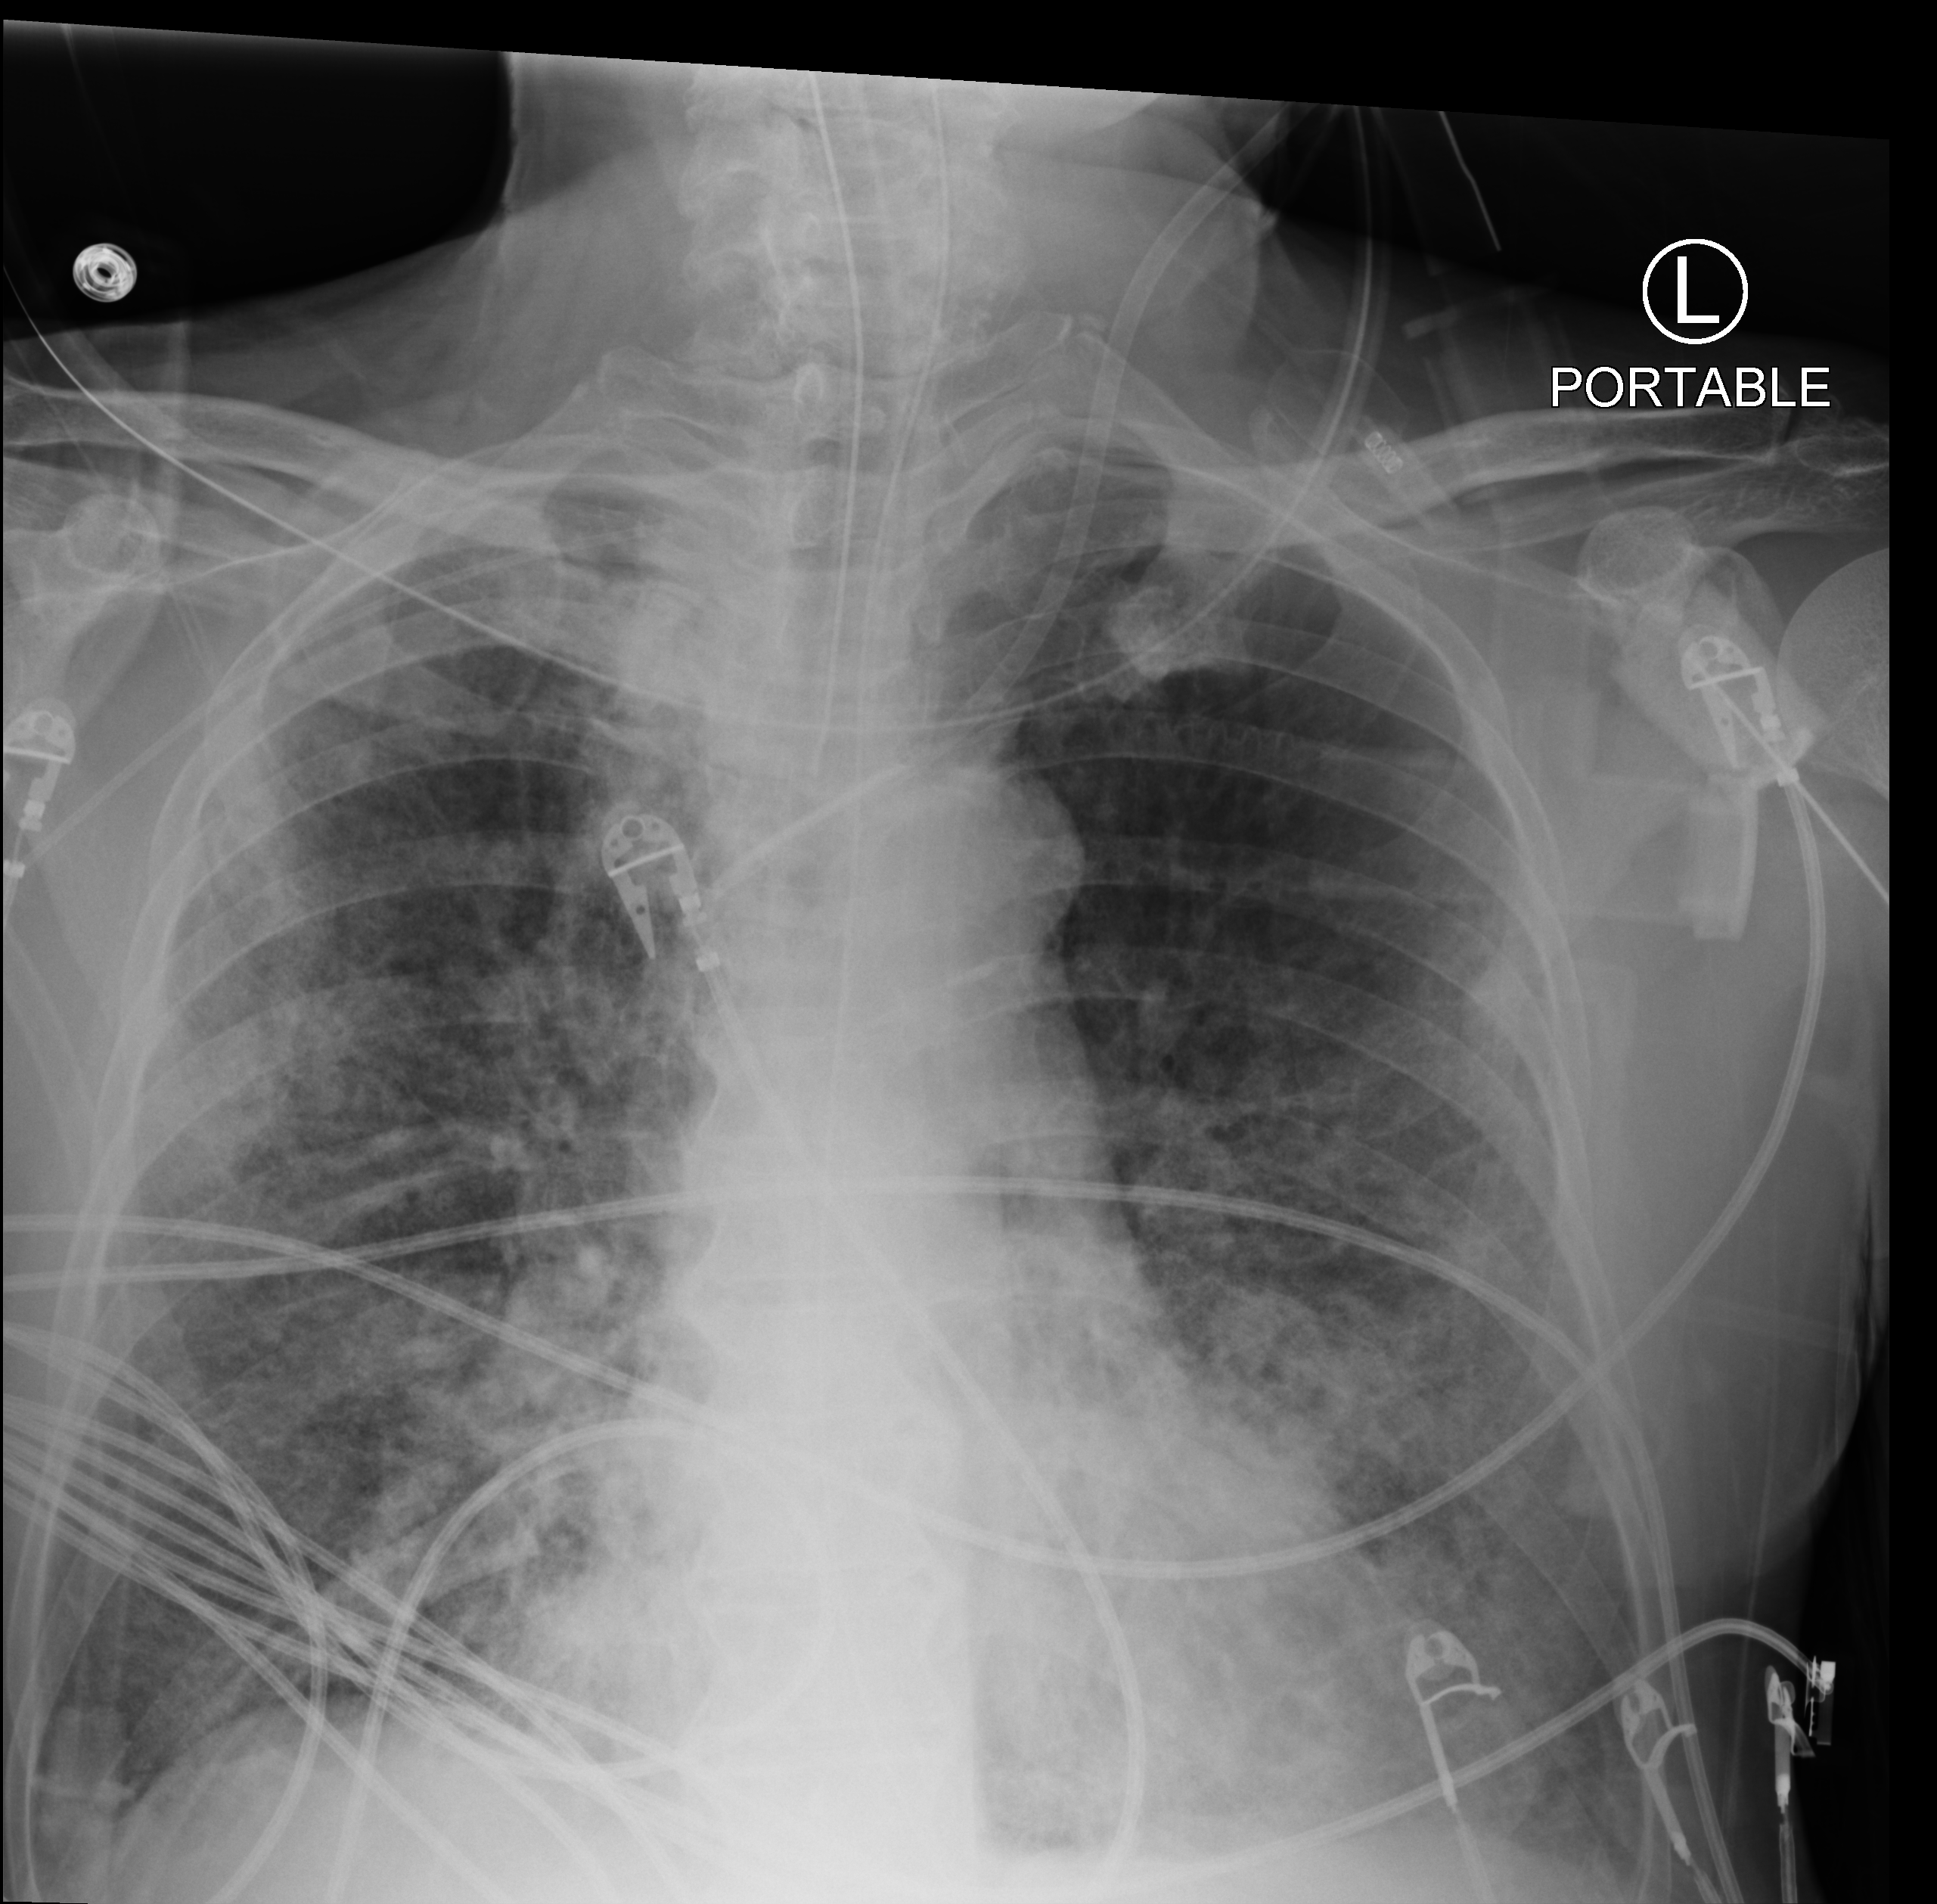
Bedside chest radiograph (computed radiography). Patient hospitalised with COVID-19; male, aged 60–74 years.
Hospital-stay facts (about this admission, not read from this image; timing relative to this image not recorded):
- length of hospital stay: 26 days
- chronic kidney disease (admission record): no
- mechanically ventilated during this hospital stay: yes